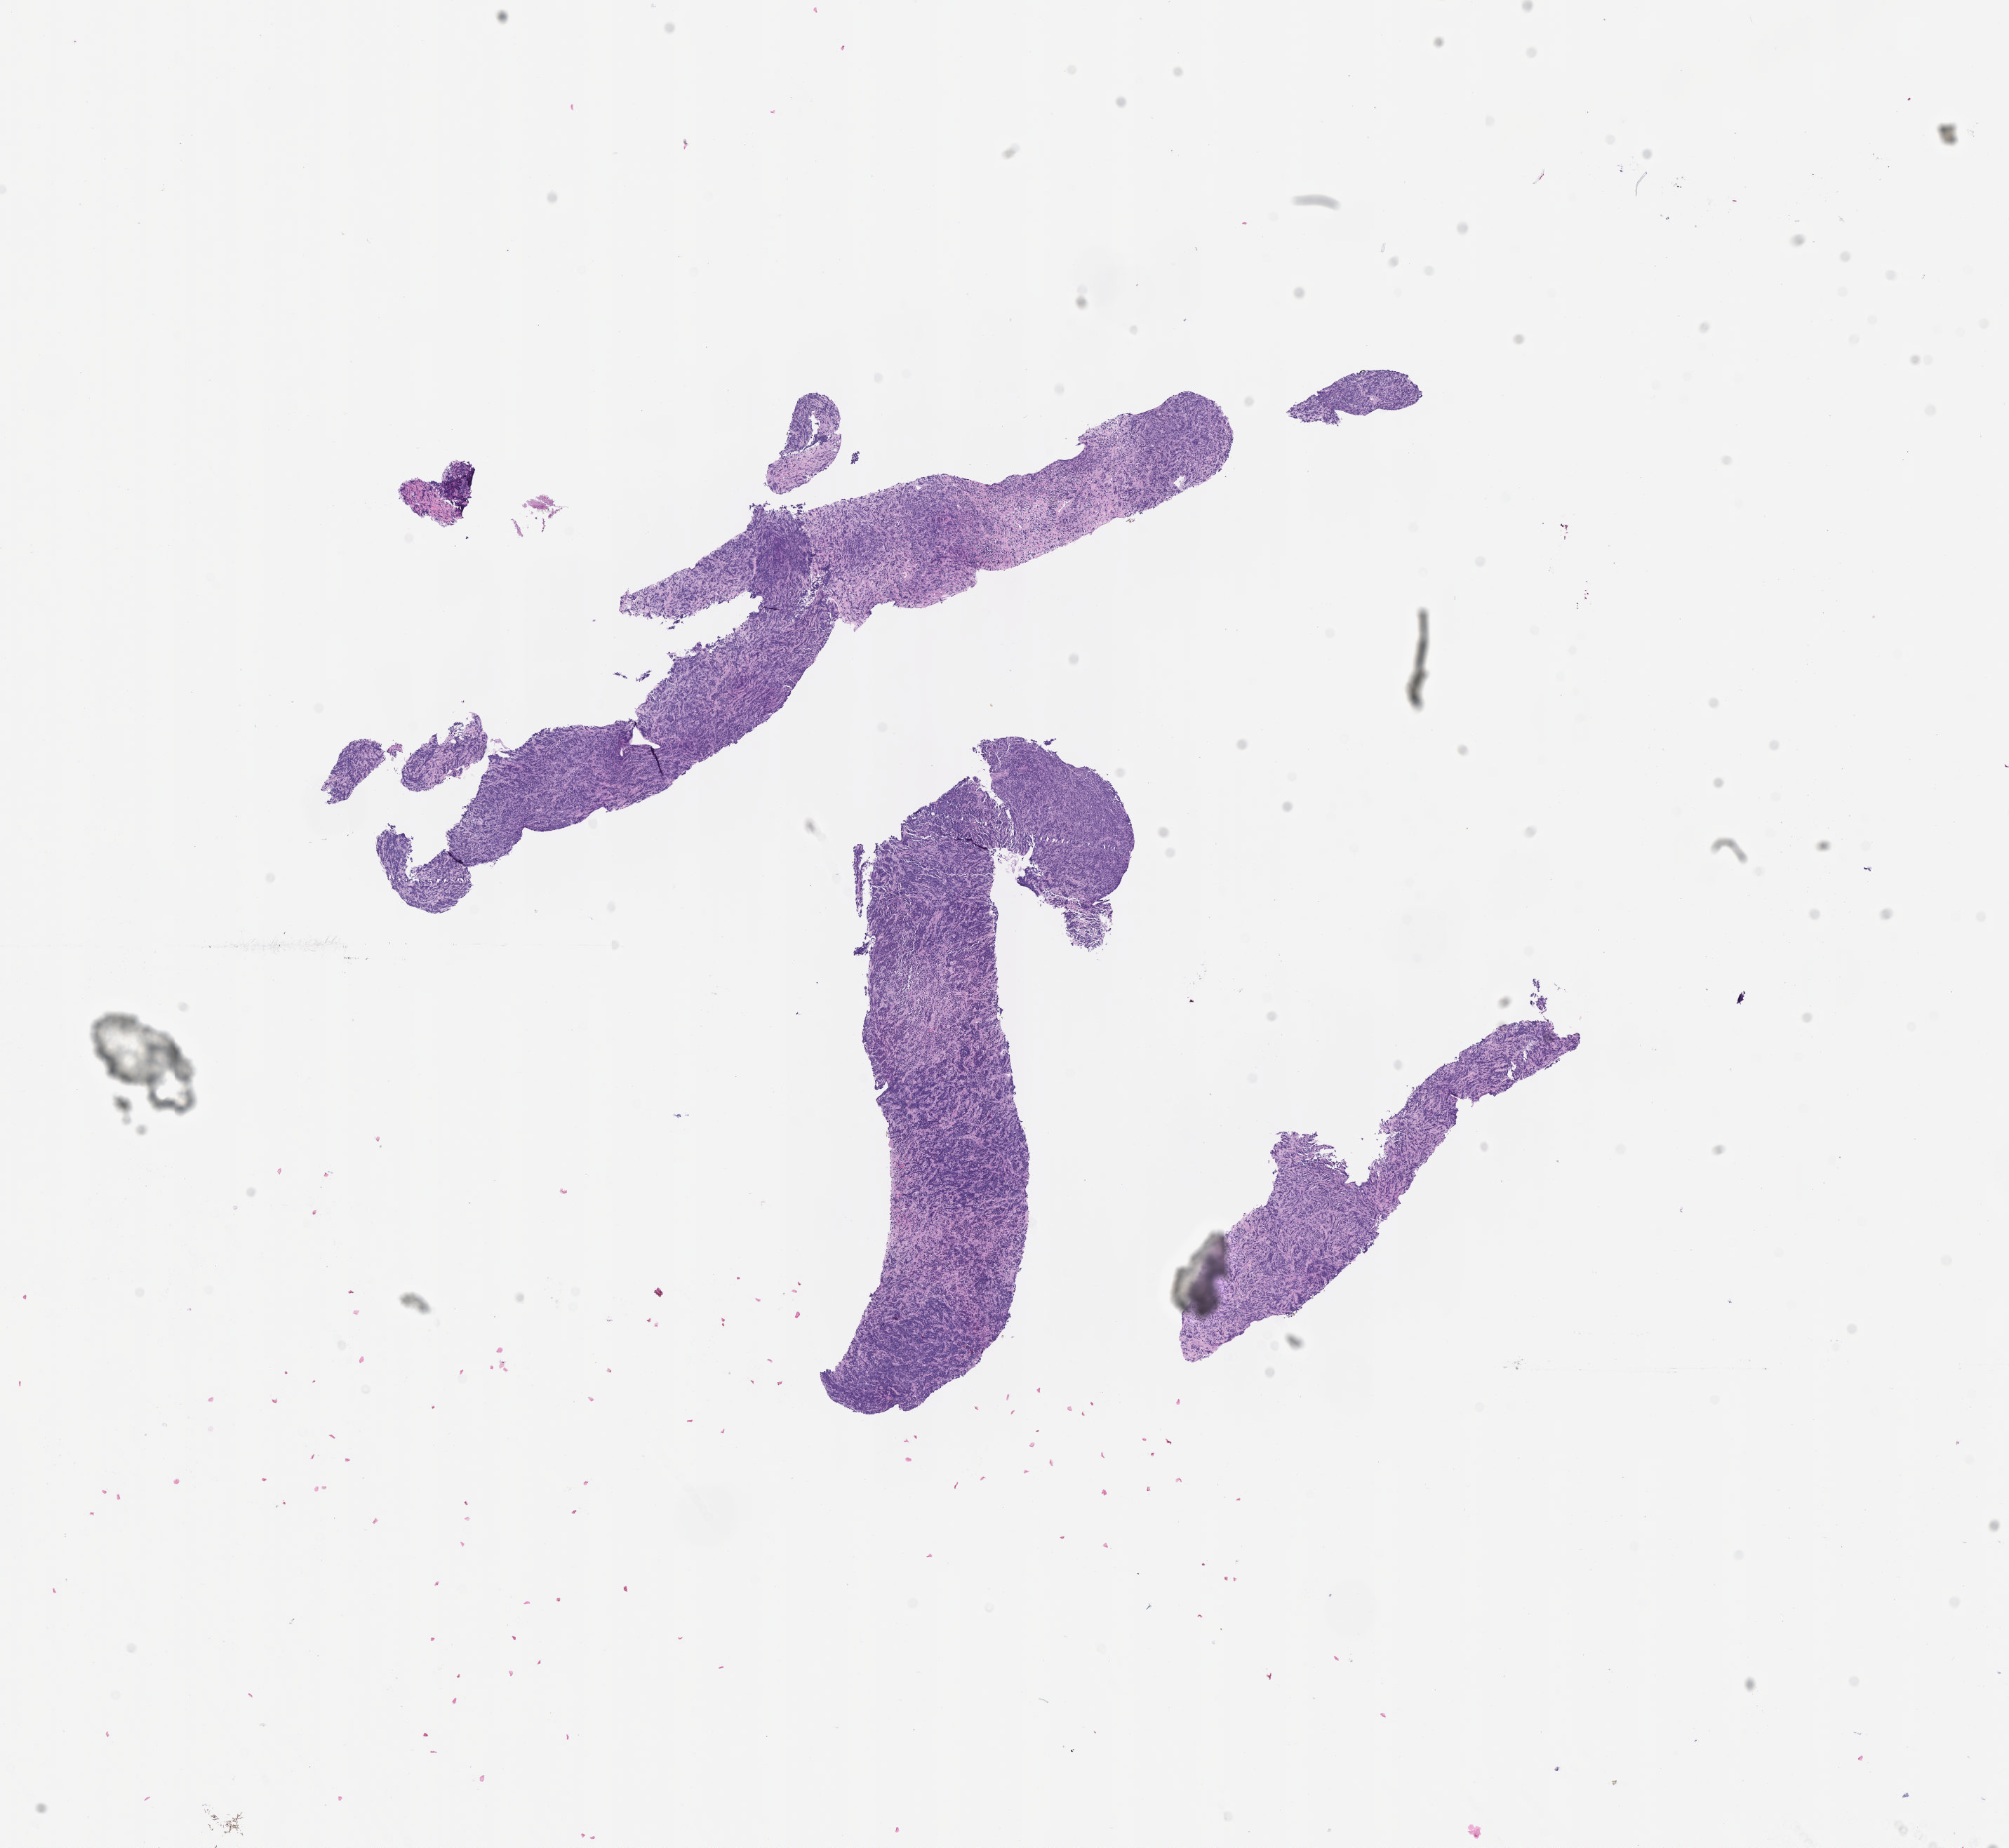
Whole-slide image, hematoxylin and eosin (H&E) stain — shown as a low-resolution overview of the whole scanned area (about 11.6 x 10.6 mm); formalin-fixed, paraffin-embedded (FFPE) tissue; specimen: primary tumor; anatomic site: abdomen proper. Male patient; age at initial diagnosis 2 years. Slide review estimates, as recorded: tumor cells 70%, tumor nuclei 90%, stromal cells 20%, necrosis 10%, normal cells 0%. Inflammatory infiltration, as recorded: lymphocyte infiltration 30%, monocyte infiltration 30%, neutrophil infiltration 10%.
Section: top of the tissue portion. Histologic diagnosis: Diffuse large B-cell lymphoma, NOS.